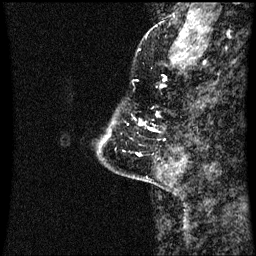
Breast MRI (dynamic contrast-enhanced), one sagittal slice; position 10 of 60 along the scan axis; dynamic contrast-enhanced series, image 2 of 3 at this slice position (ordered by acquisition); 1.5 T; TE 4.2 ms, TR 8.9 ms; 2 mm slice thickness; 256 × 256 image matrix. Patient: female, 43 years. Case-level facts recorded for this patient, not image findings: setting: breast cancer imaged before/during neoadjuvant chemotherapy; receptor status: HR-positive, HER2-negative.
Structures marked on this image (semi-automatically segmented with operator editing):
- analysis volume of interest (the breast-tissue region the enhancement analysis was run in; not a lesion): bounding box (x1, y1, x2, y2) in pixels: (110, 122, 156, 137)
- tumour enhancement mask (voxels above the 70 % enhancement threshold inside the analysis volume of interest): (150, 128, 152, 131)